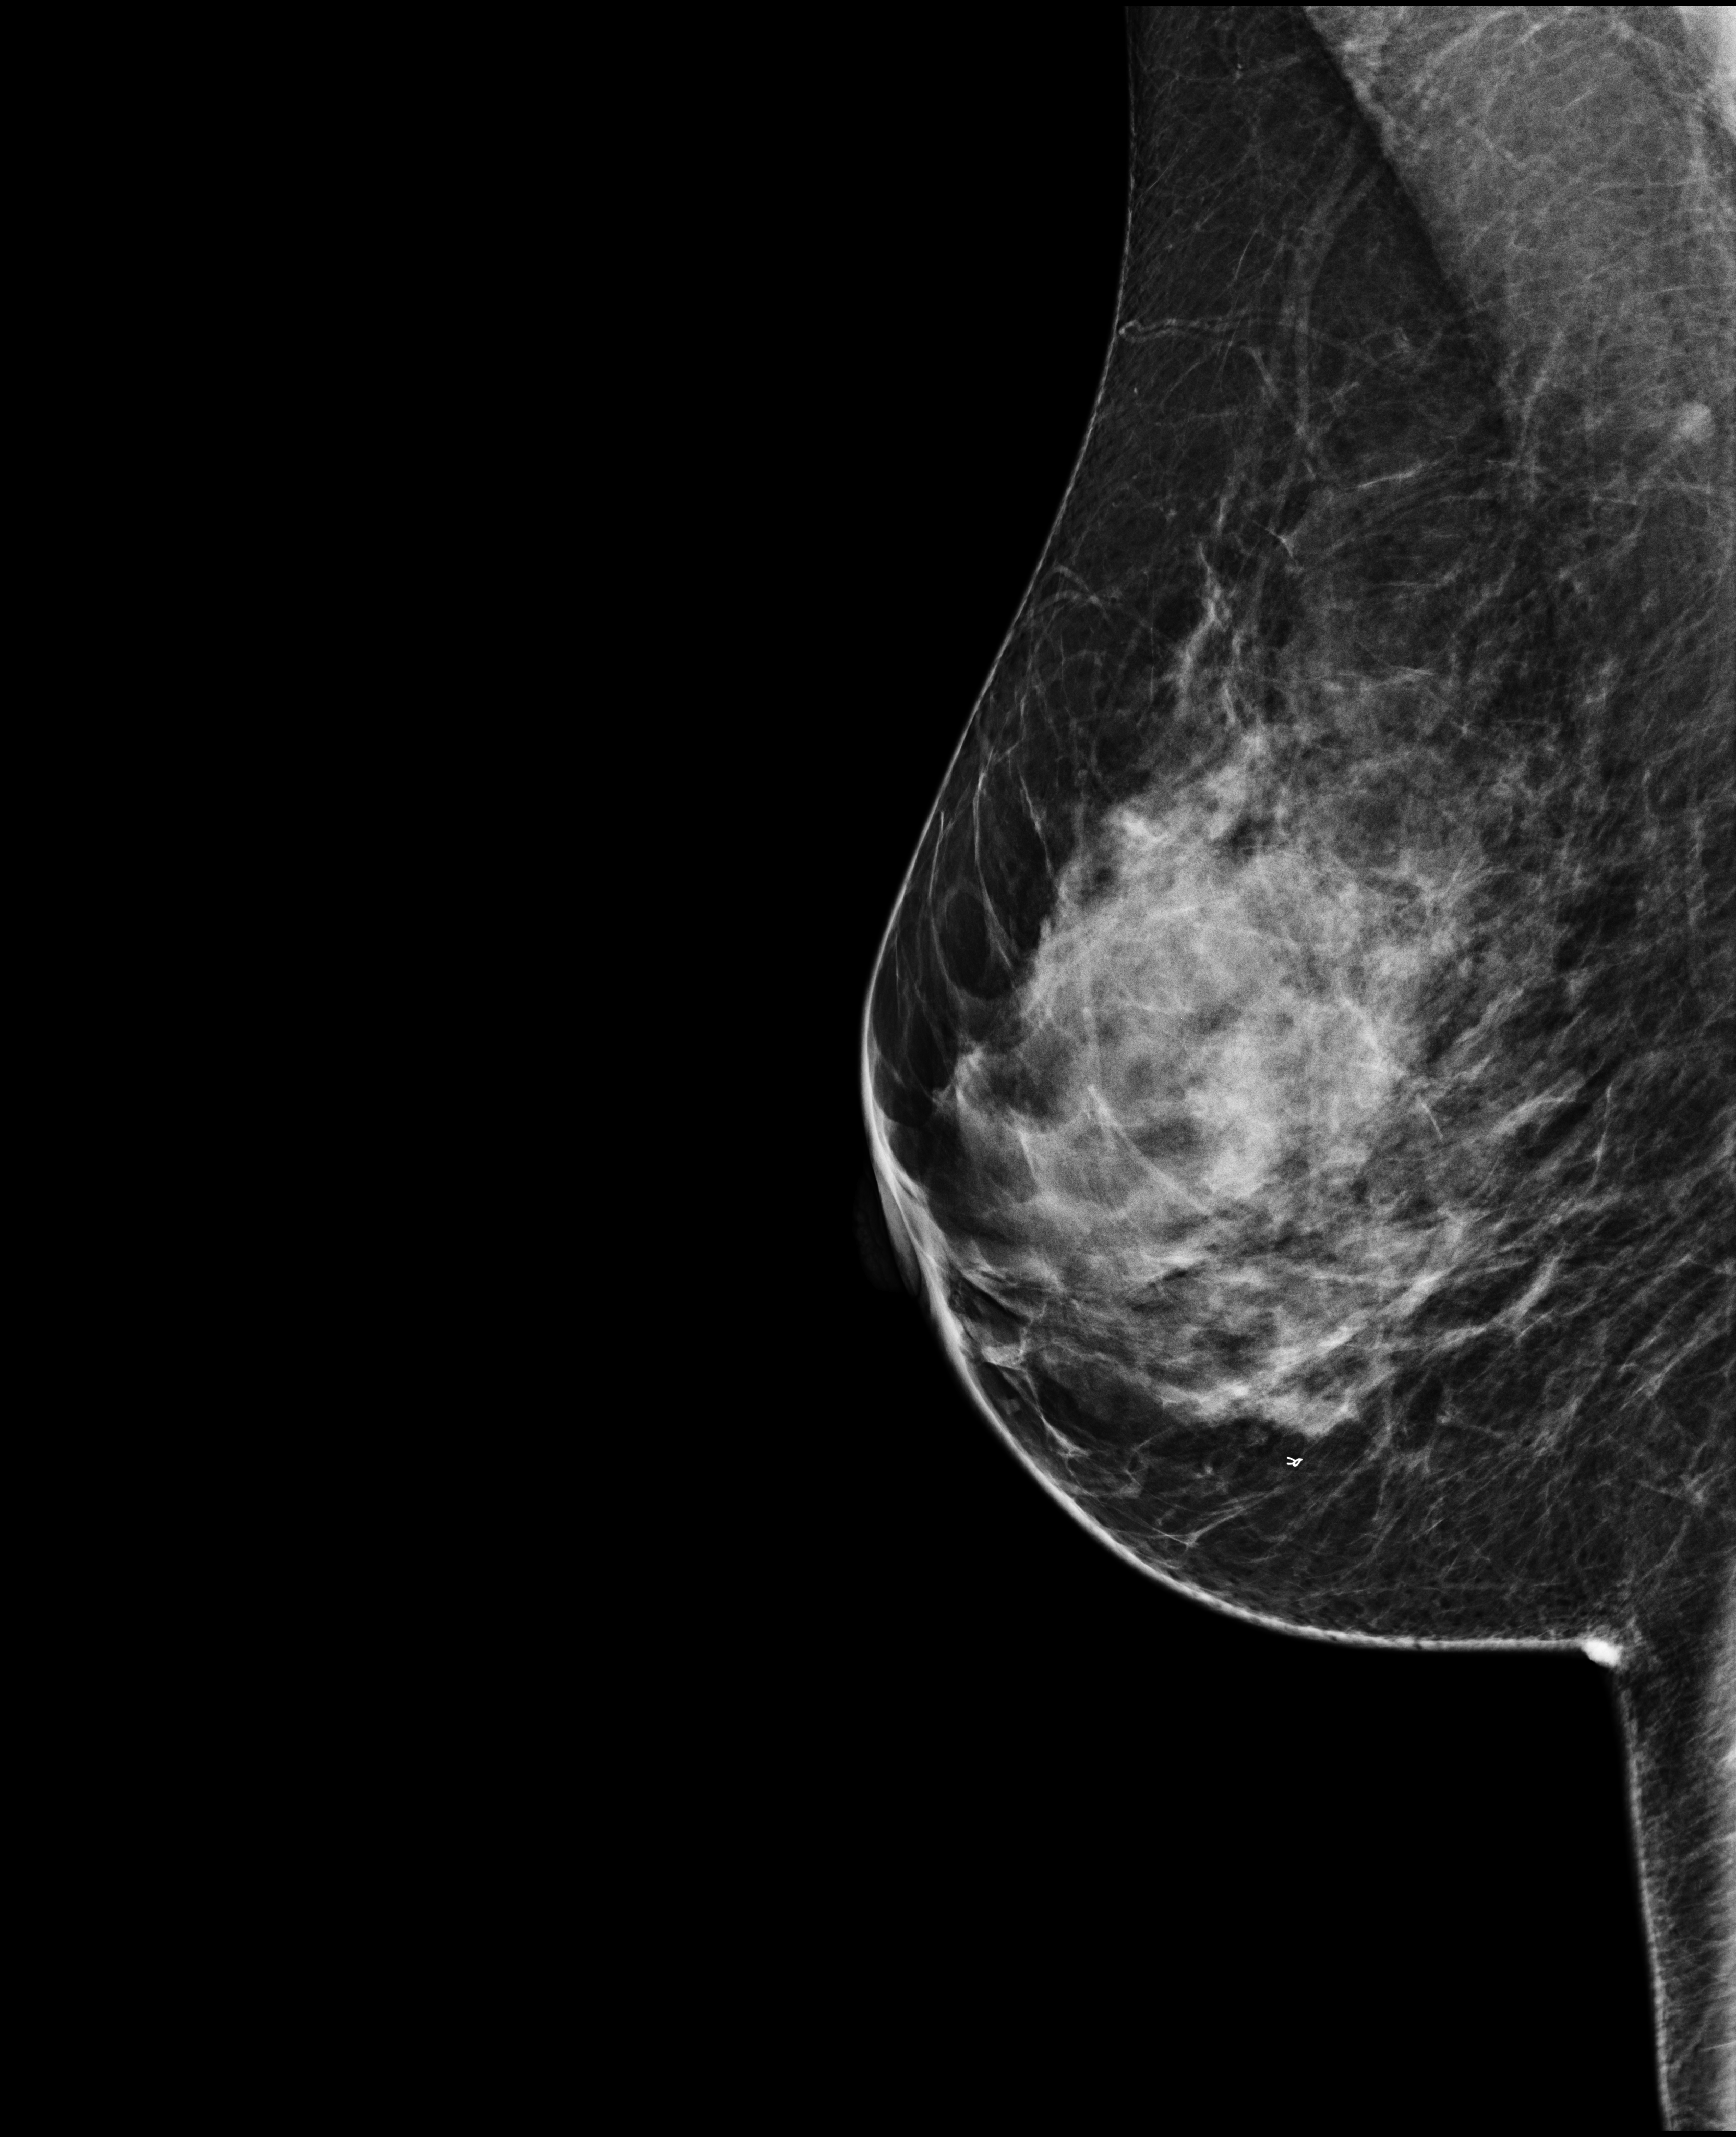
Digital mammogram (FFDM), right breast, mediolateral oblique (MLO) view, screening examination, compressed breast thickness 62 mm. Female patient, age 46 years.
Breast density at the screening exam (both breasts): heterogeneously dense (BI-RADS density category c). Final BI-RADS assessment for this screening round (tomosynthesis exam, both breasts): category 5. Recall: no recall after this screen.